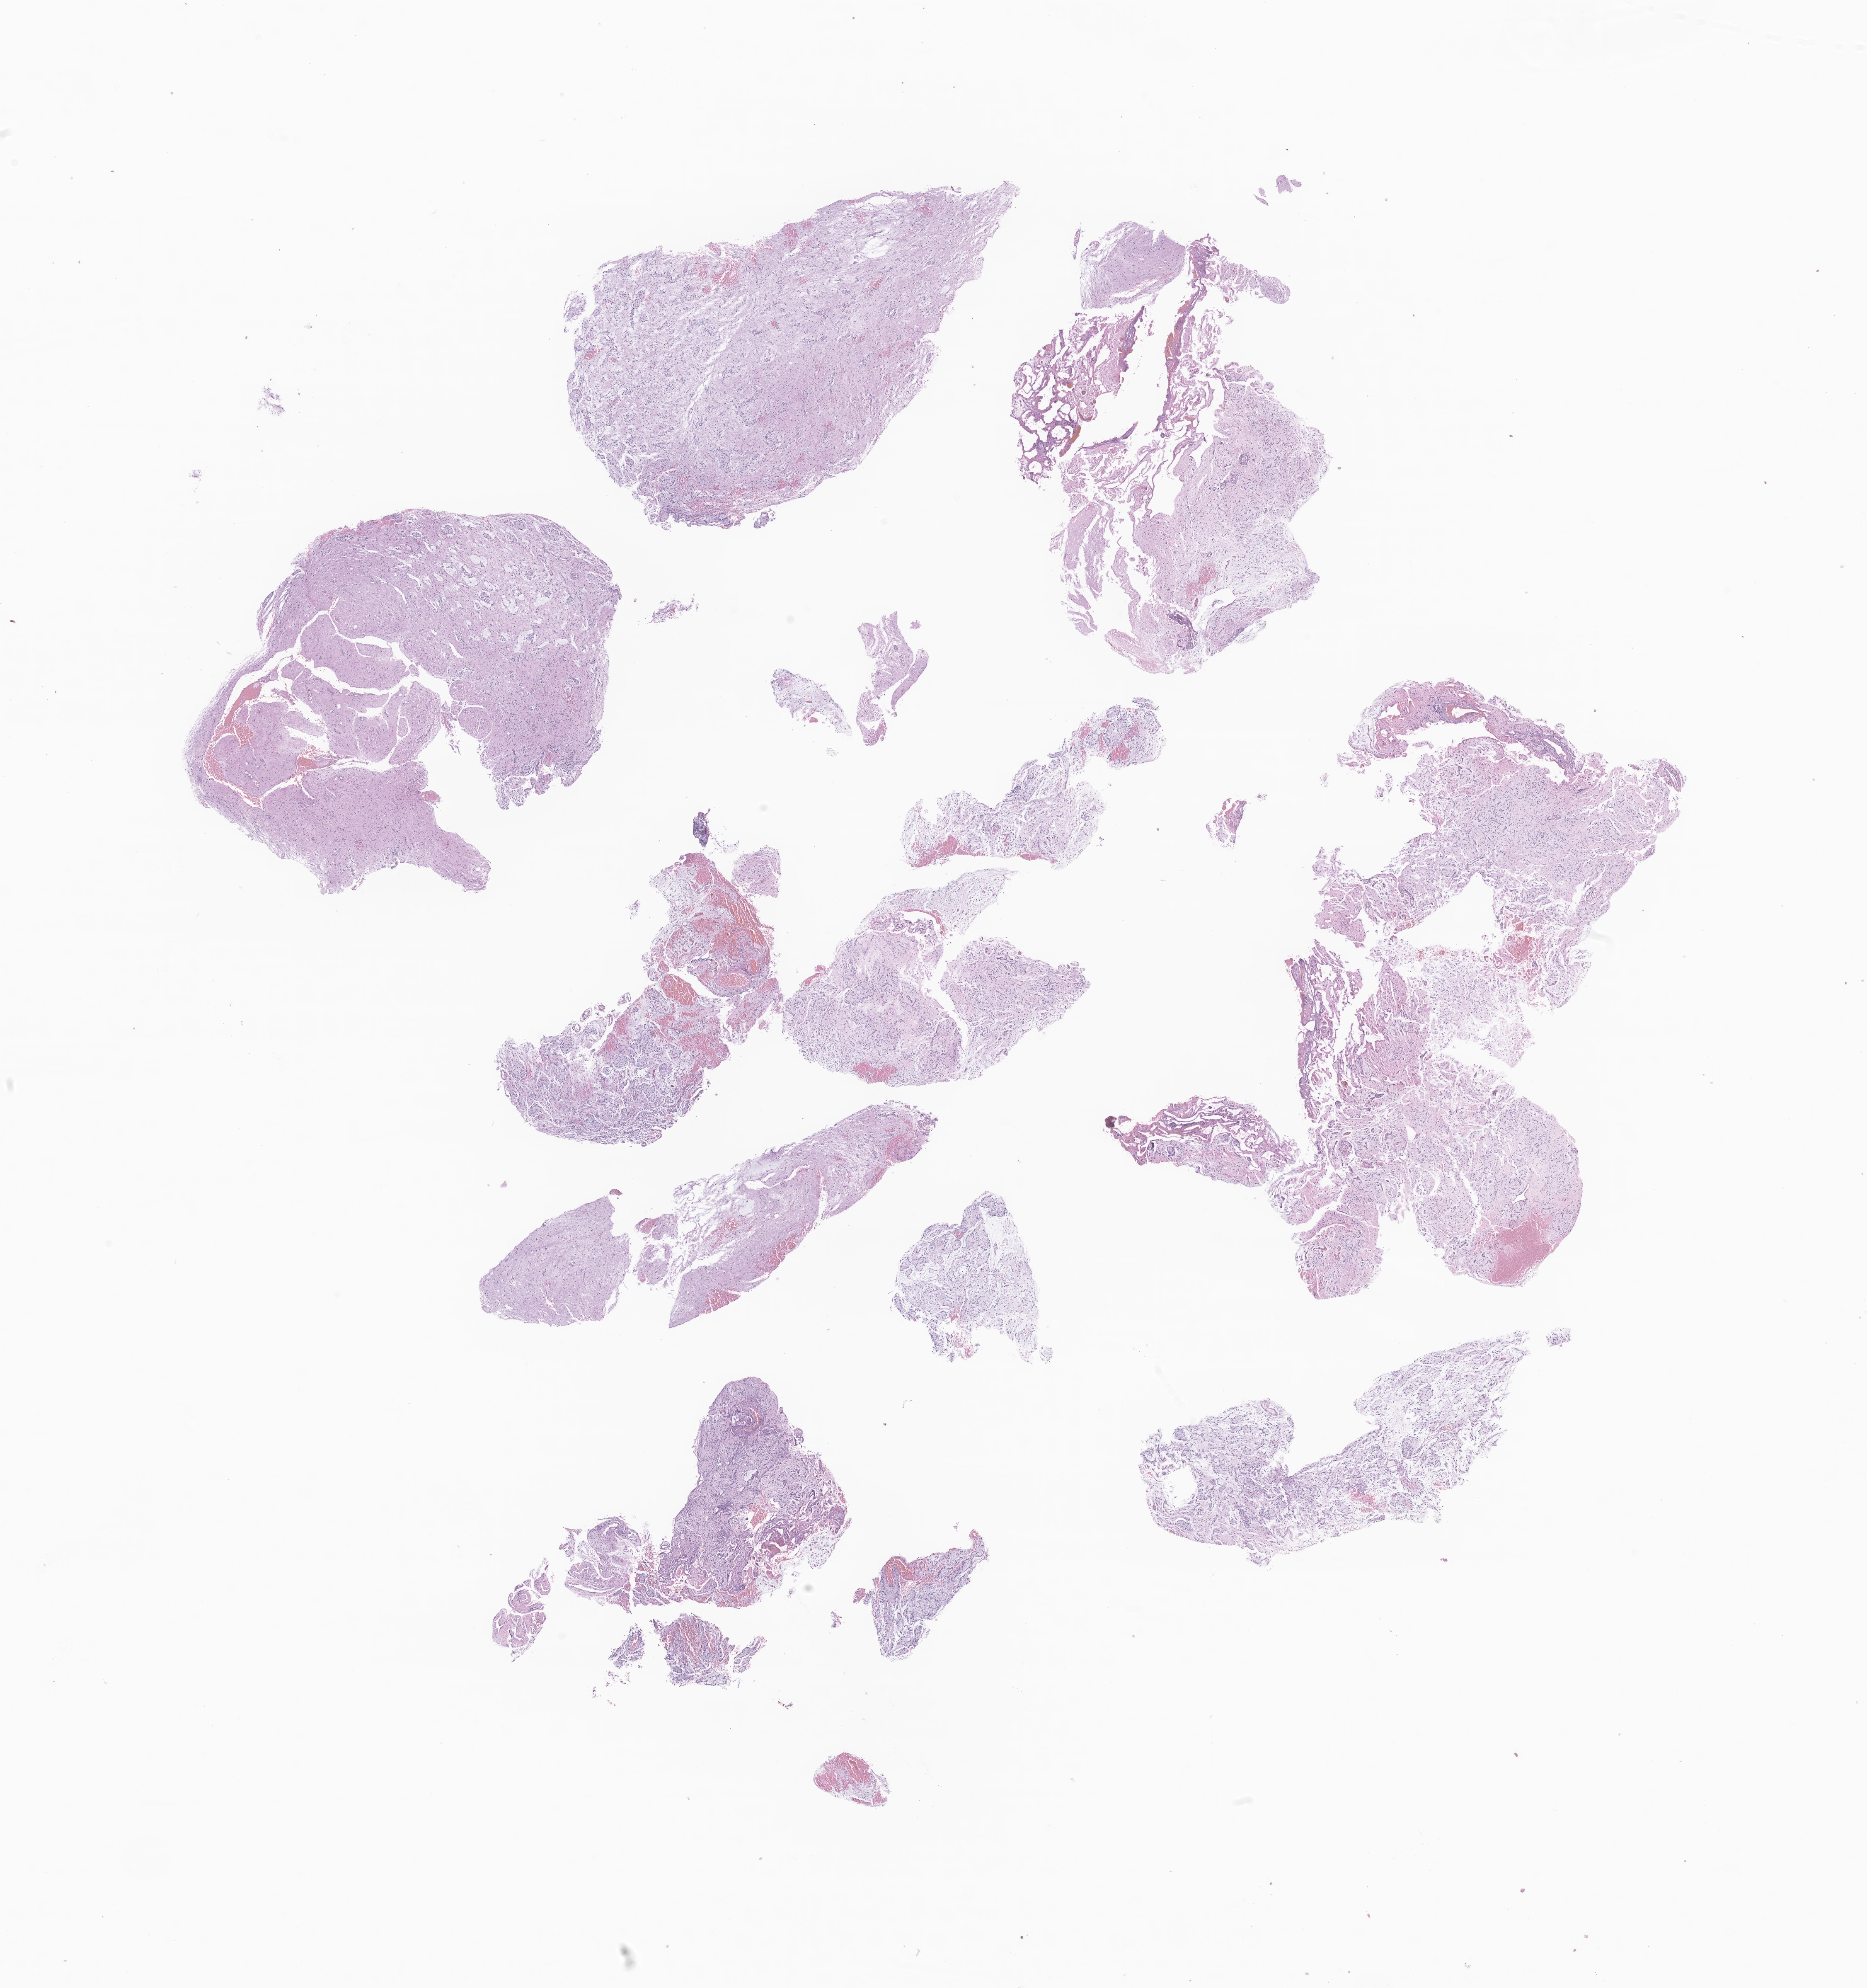
Digitized H&E-stained section of tumor tissue from the temporal lobe — a low-resolution overview of the entire scanned area, about 19.0 x 20.2 mm. FFPE section. Patient male; age 197 months (16 years 5 months).
Diagnosis (ICD-O-3 morphology term): Pilocytic astrocytoma.